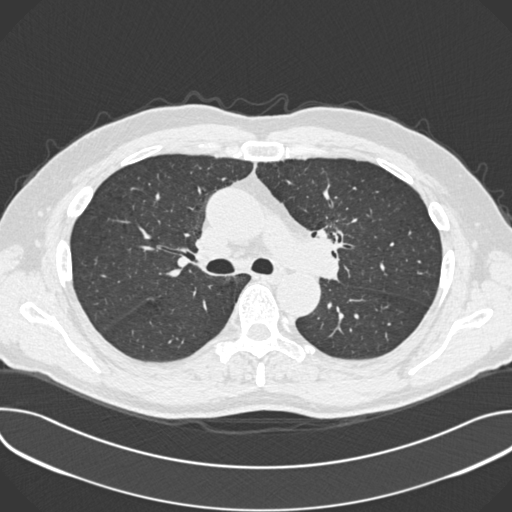
Low-dose screening chest CT, one axial slice. Slice 241 of 361 in the series (ordered by position). Reconstruction kernel B30f. 120 kVp. Lung window (W 1500 / L -600 HU). 512 × 512 image matrix, field of view 380 × 380 mm.
Annotated regions visible in this slice (expert manual segmentation):
- lesion 1 (tumor, upper lobe of left lung): box from (x=316, y=229) to (x=344, y=251) px